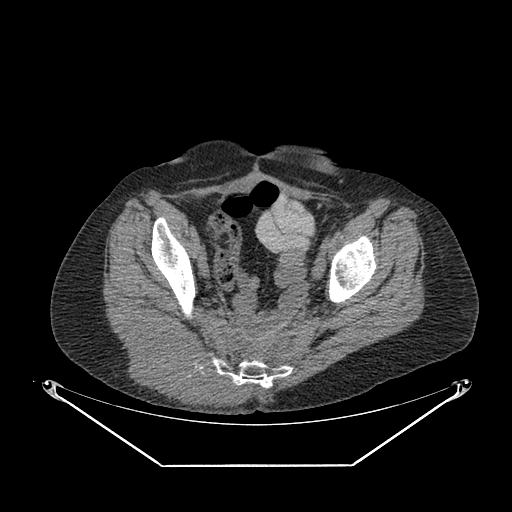
CT of an extremity soft-tissue mass (from a PET/CT study), one axial slice. Position 64 of 267 along the scan axis. 140 kVp. Soft-tissue window (W 400 / L 40 HU). 3.75 mm slice thickness. 512 × 512 image matrix, field of view 500 × 500 mm. Female patient. Case-level facts recorded for this patient, not image findings: histological type: spindle cell suggestive of myxofibrosarcoma; grade: intermediate; site of the primary tumour: right buttock.
Annotated regions visible in this slice (expert contour drawn on MRI and transferred to this co-registered scan by the dataset authors):
- gross tumour volume (mass): bounding box [x1, y1, x2, y2] px = [121, 322, 247, 408]